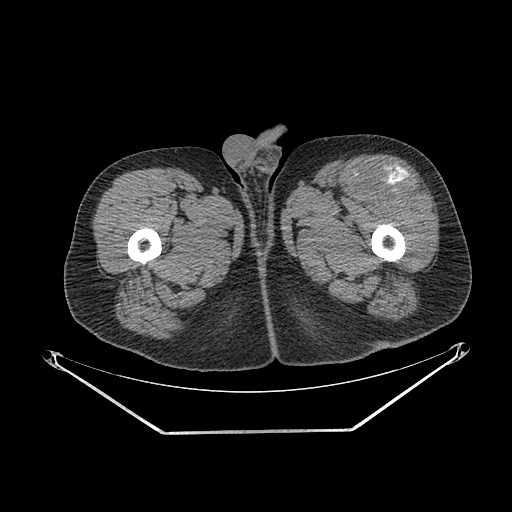
CT of an extremity soft-tissue mass (from a PET/CT study), one axial slice. Position 255 of 267 along the scan axis. Soft-tissue window (W 400 / L 40 HU). 3.75 mm slice thickness. 512 × 512 image matrix, field of view 500 × 500 mm. Male patient. From the clinical record (not read from this slice): histological type: extraskeletal osteosarcoma; grade: high; site of the primary tumour: thigh.
Outlined on this slice (expert contour drawn on MRI and transferred to this co-registered scan by the dataset authors):
- gross tumour volume (mass): bounding box [x1, y1, x2, y2] px = [365, 169, 419, 197]